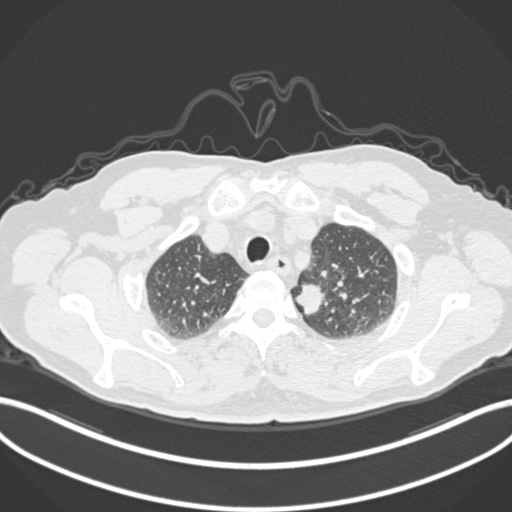
Chest CT, one axial slice; position 273 of 306 along the scan axis; reconstruction kernel B30f; 120 kVp; lung window (W 1500 / L -600 HU); 1 mm slice thickness; 512 × 512 image matrix. Patient: male, 64 years. Case-level facts recorded for this patient, not image findings: clinical TNM (as recorded): T1c N0 M0.
Outlined on this slice (bounding box drawn by a radiologist):
- lung tumour (recorded histology: adenocarcinoma): bounding box <292,280,330,320> (left, top, right, bottom; pixels)